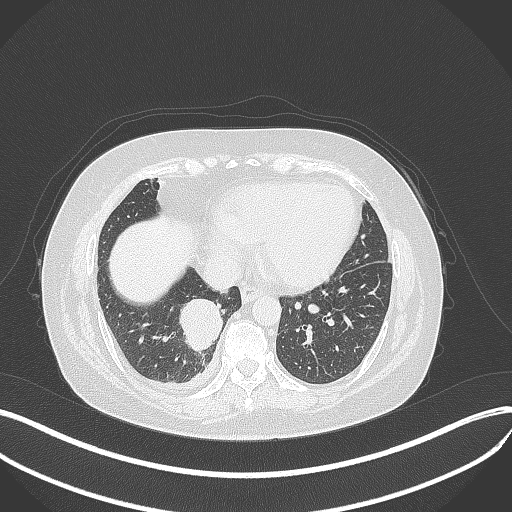
Chest CT, one axial slice; 120 kVp; lung window (W 1500 / L -600 HU); 1 mm slice thickness; 512 × 512 image matrix, field of view 400 × 400 mm. Female patient, age 56 years. From the clinical record (not read from this slice): clinical TNM (as recorded): T2b N1 M0.
Outlined on this slice (rectangle marked by the reading radiologist):
- lung tumour (recorded histology: small cell carcinoma): bounding box [x1, y1, x2, y2] px = [178, 297, 225, 353]